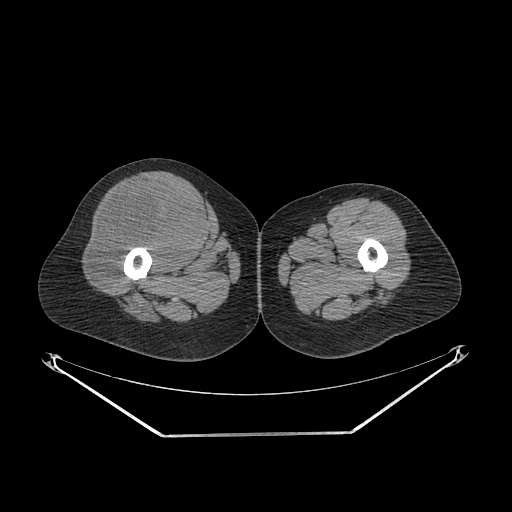
CT of an extremity soft-tissue mass (from a PET/CT study), one axial slice. Position 253 of 311 along the scan axis. Soft-tissue window (W 400 / L 40 HU). 3.75 mm slice thickness. 512 × 512 image matrix. Female patient. Case-level facts recorded for this patient, not image findings: histological type: pleiomorphic undifferentiated sarcoma; grade: high; site of the primary tumour: right quadricep.
Structures marked on this image (expert contour drawn on MRI and transferred to this co-registered scan by the dataset authors):
- tumour plus oedema (research contour): bounding box [x1, y1, x2, y2] px = [91, 183, 200, 289]
- tumour (research contour): [91, 183, 200, 289]